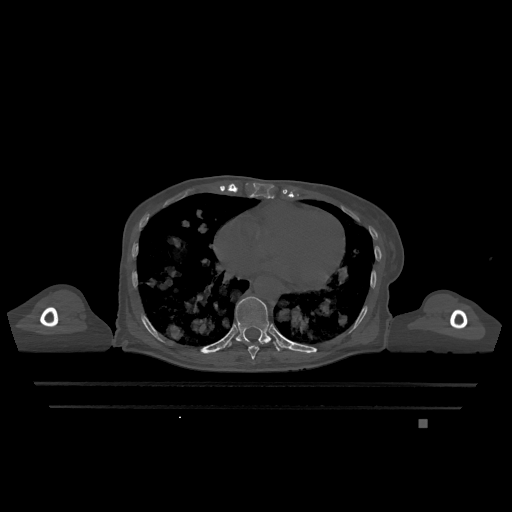
CT including the spine, one axial slice; position 663 of 1317 along the scan axis; bone window (W 1800 / L 400 HU); 512 × 512 image matrix, field of view 500 × 500 mm. Female patient, age 74 years. Case-level facts recorded for this patient, not image findings: primary cancer: lung; vertebrae with lytic lesions (as recorded): T1, T4, T5, T6, L4, L5.
Annotated regions visible in this slice (semi-automatic segmentation, software-assisted and operator-edited):
- T10 vertebra: box from (x=229, y=296) to (x=281, y=352) px
- T9 vertebra: (x=248, y=345)–(x=259, y=360)